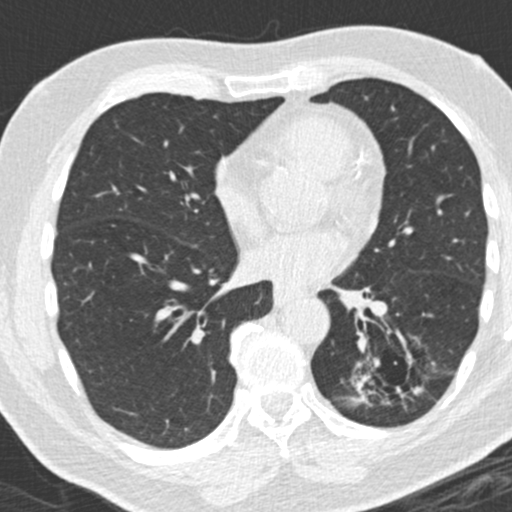
Chest CT (low-dose screening protocol), one axial image, third annual screen, lung window (W 1500 / L -600 HU), 2 mm slice thickness. Male participant, aged 66 years at enrolment.
• Expert reader's lesion annotation, box from (x=355, y=347) to (x=426, y=429) px.
• Reader record for this screening exam (exam-level; its link to the box is not recorded): non-calcified nodule or mass ≥4 mm, left lower lobe, 31 × 24 mm, spiculated (stellate) margins, pre-existing on the prior screen: yes; interval growth: yes.
• Participant outcome: lung cancer diagnosed 56 days after this screen — adenocarcinoma, NOS, left lower lobe, poorly differentiated (G3), stage IB (AJCC 6th edition), 38 mm at pathology.